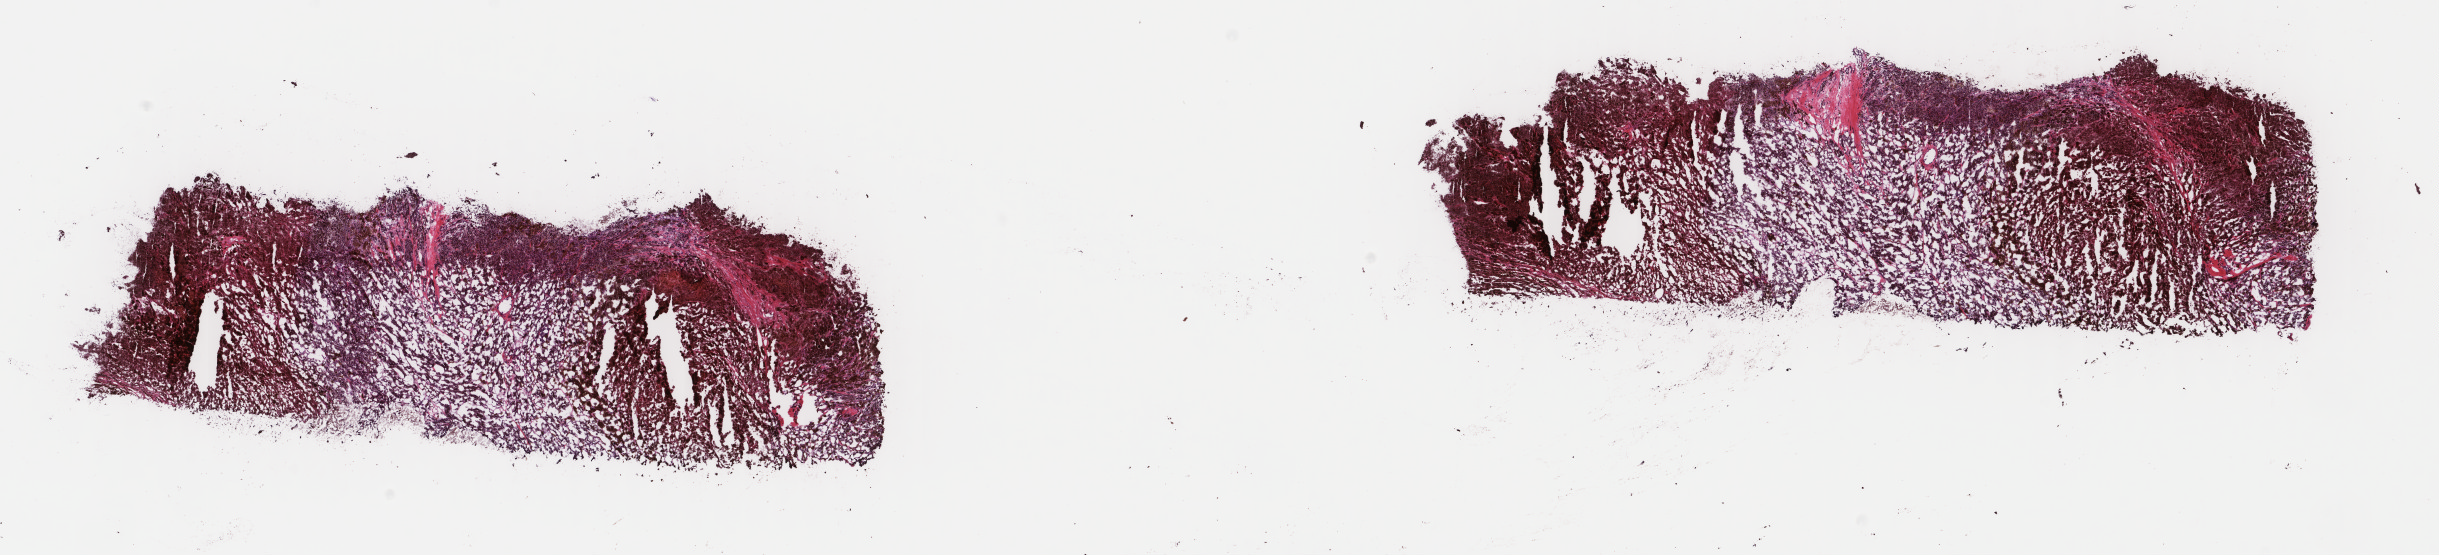
Digitized H&E tissue section (whole slide) — a low-resolution overview of the entire scanned area, about 19.4 x 4.4 mm, frozen section from the top of the tissue portion, primary tumour sample from the skin. Male, age 70 years at initial diagnosis. Composition of this section per pathologist review: tumour cells 85%, tumour nuclei 85%.
Diagnosis: Superficial spreading melanoma.